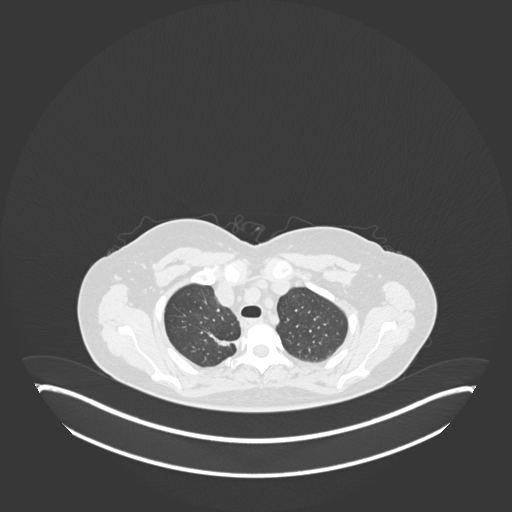
Chest CT, one axial slice; slice 148 of 181 in the series (ordered by position); 120 kVp; lung window (W 1500 / L -600 HU); 1 mm slice thickness; 512 × 512 image matrix, field of view 500 × 500 mm. Female patient, age 65 years. From the clinical record (not read from this slice): clinical TNM (as recorded): T1b N0 M0.
Annotated regions visible in this slice (bounding box drawn by a radiologist):
- lung tumour (recorded histology: adenocarcinoma): bounding box [x1, y1, x2, y2] px = [204, 325, 235, 352]